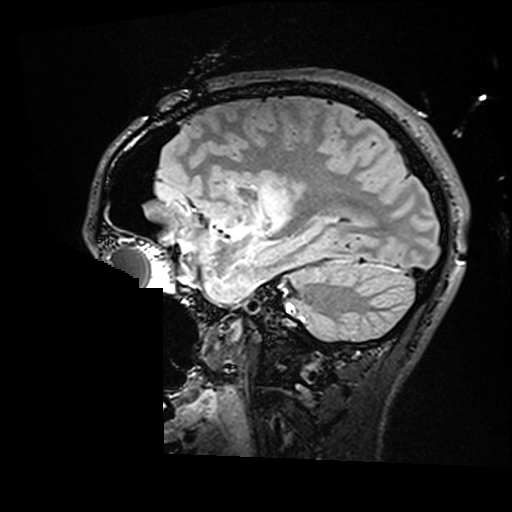
Brain MRI from a brain-tumour surgery series, one sagittal slice; slice 113 of 176 in the series (ordered by position); T2 FLAIR; 1 mm slice thickness; 512 × 512 image matrix, field of view 250 × 250 mm. From the clinical record (not read from this slice): histopathology: Astrocytoma; WHO grade: 2; IDH mutation: yes; tumour location: Right Insular.
Structures marked on this image (expert manual segmentation):
- residual tumour: bounding box <260,183,287,228> (left, top, right, bottom; pixels)